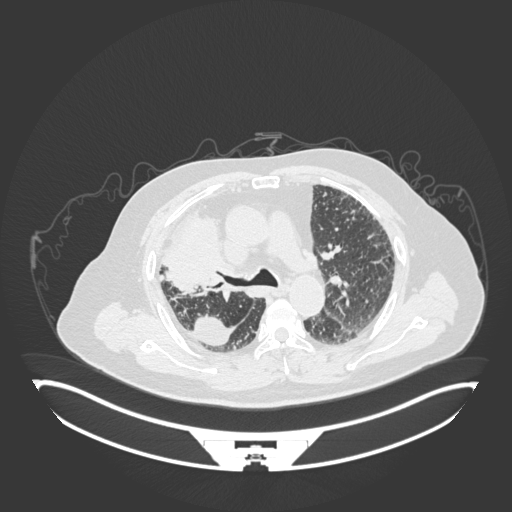
Chest CT, one axial slice; position 120 of 201 along the scan axis; reconstruction kernel B30f; 120 kVp; lung window (W 1500 / L -600 HU); 1 mm slice thickness; 512 × 512 image matrix. Male patient, age 69 years. From the clinical record (not read from this slice): clinical TNM (as recorded): T4 N3 M1.
Annotated regions visible in this slice (rectangle marked by the reading radiologist):
- lung tumour (recorded histology: adenocarcinoma): bounding box <155,205,226,295> (left, top, right, bottom; pixels)